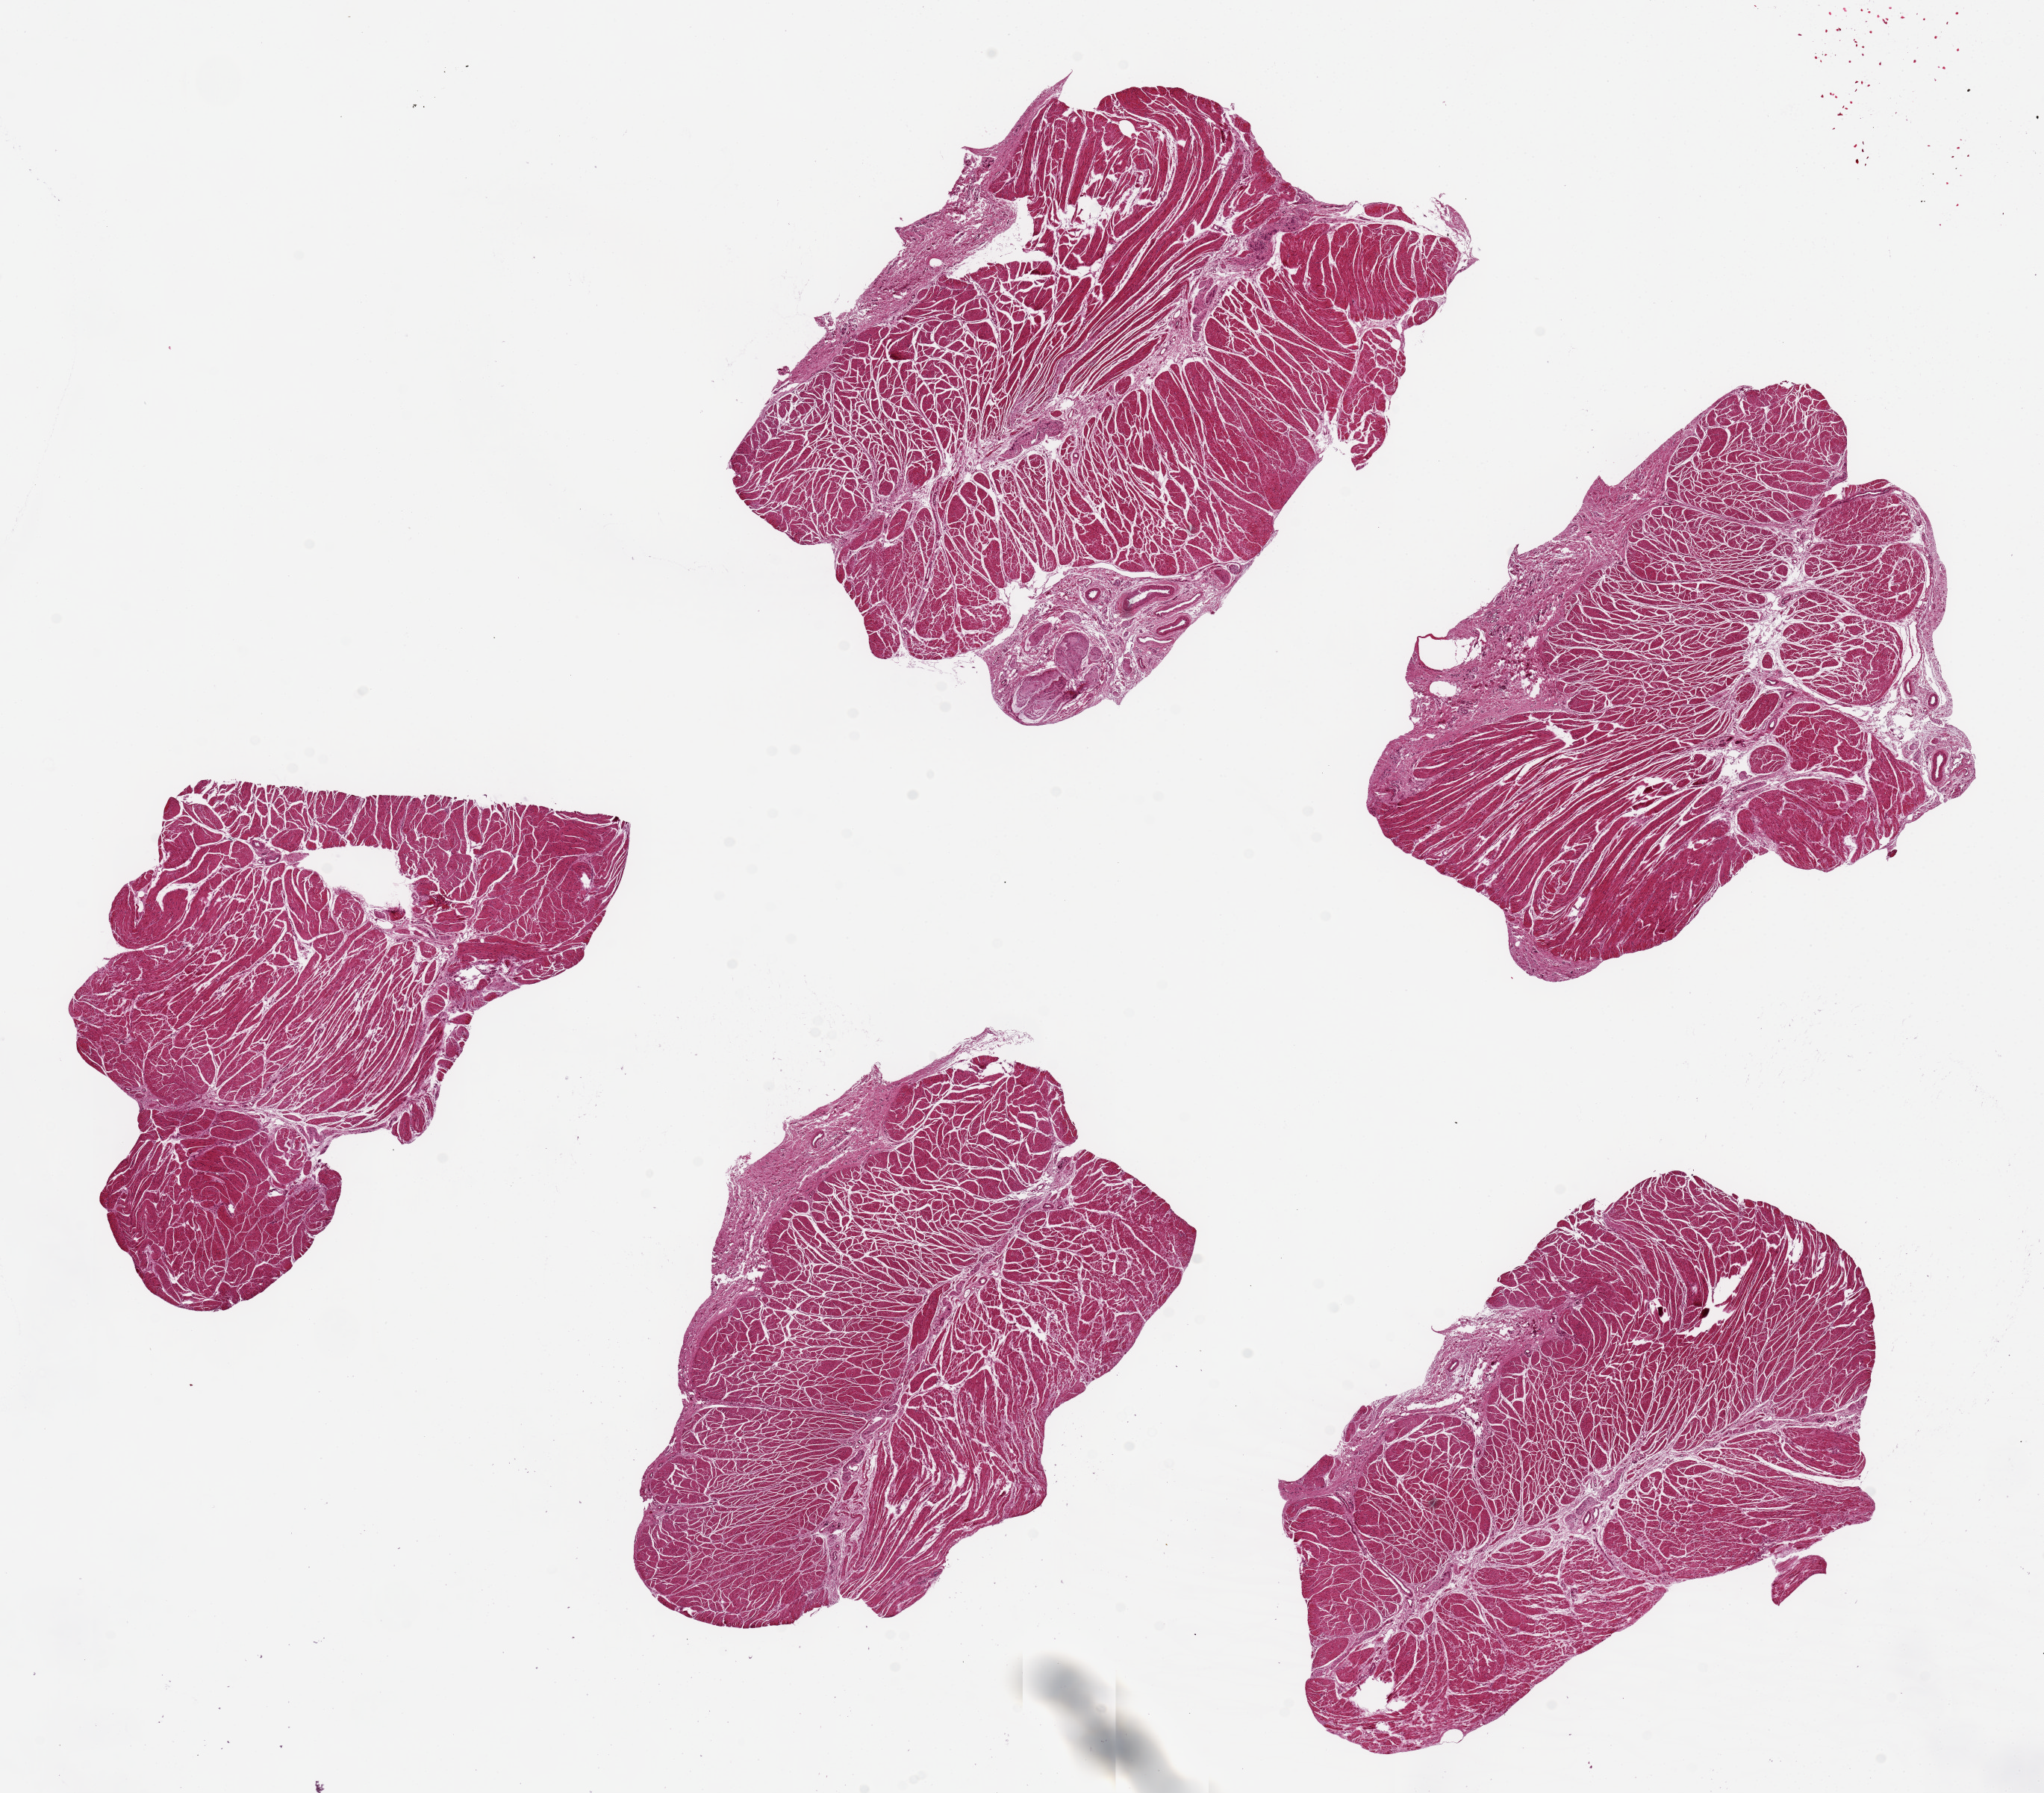
Digitized H&E-stained section — a low-resolution overview of the entire scanned area, about 21.7 x 19.0 mm (from a 20x scan); PAXgene-fixed, paraffin-embedded tissue; sampled site (target tissue): esophageal muscle; donor tissue sample. Female donor.
Review note (as recorded): 5 pieces up to 7x5mm.